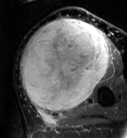
MRI of an extremity soft-tissue mass, one axial slice. Position 37 of 87 along the scan axis. T2-weighted fat-saturated. MR volume resampled by the dataset authors to the PET/CT grid (not the native acquisition matrix). 3.27 mm slice thickness. 127 × 138 image matrix, field of view 124 × 135 mm. Female patient. From the clinical record (not read from this slice): histological type: pleiomorphic leiomyosarcoma; grade: high; site of the primary tumour: left biceps.
Annotated regions visible in this slice (expert contour drawn on MRI and transferred to this co-registered scan by the dataset authors):
- gross tumour volume including surrounding oedema: bounding box [x1, y1, x2, y2] px = [20, 18, 110, 113]
- gross tumour volume (mass): [20, 20, 110, 113]